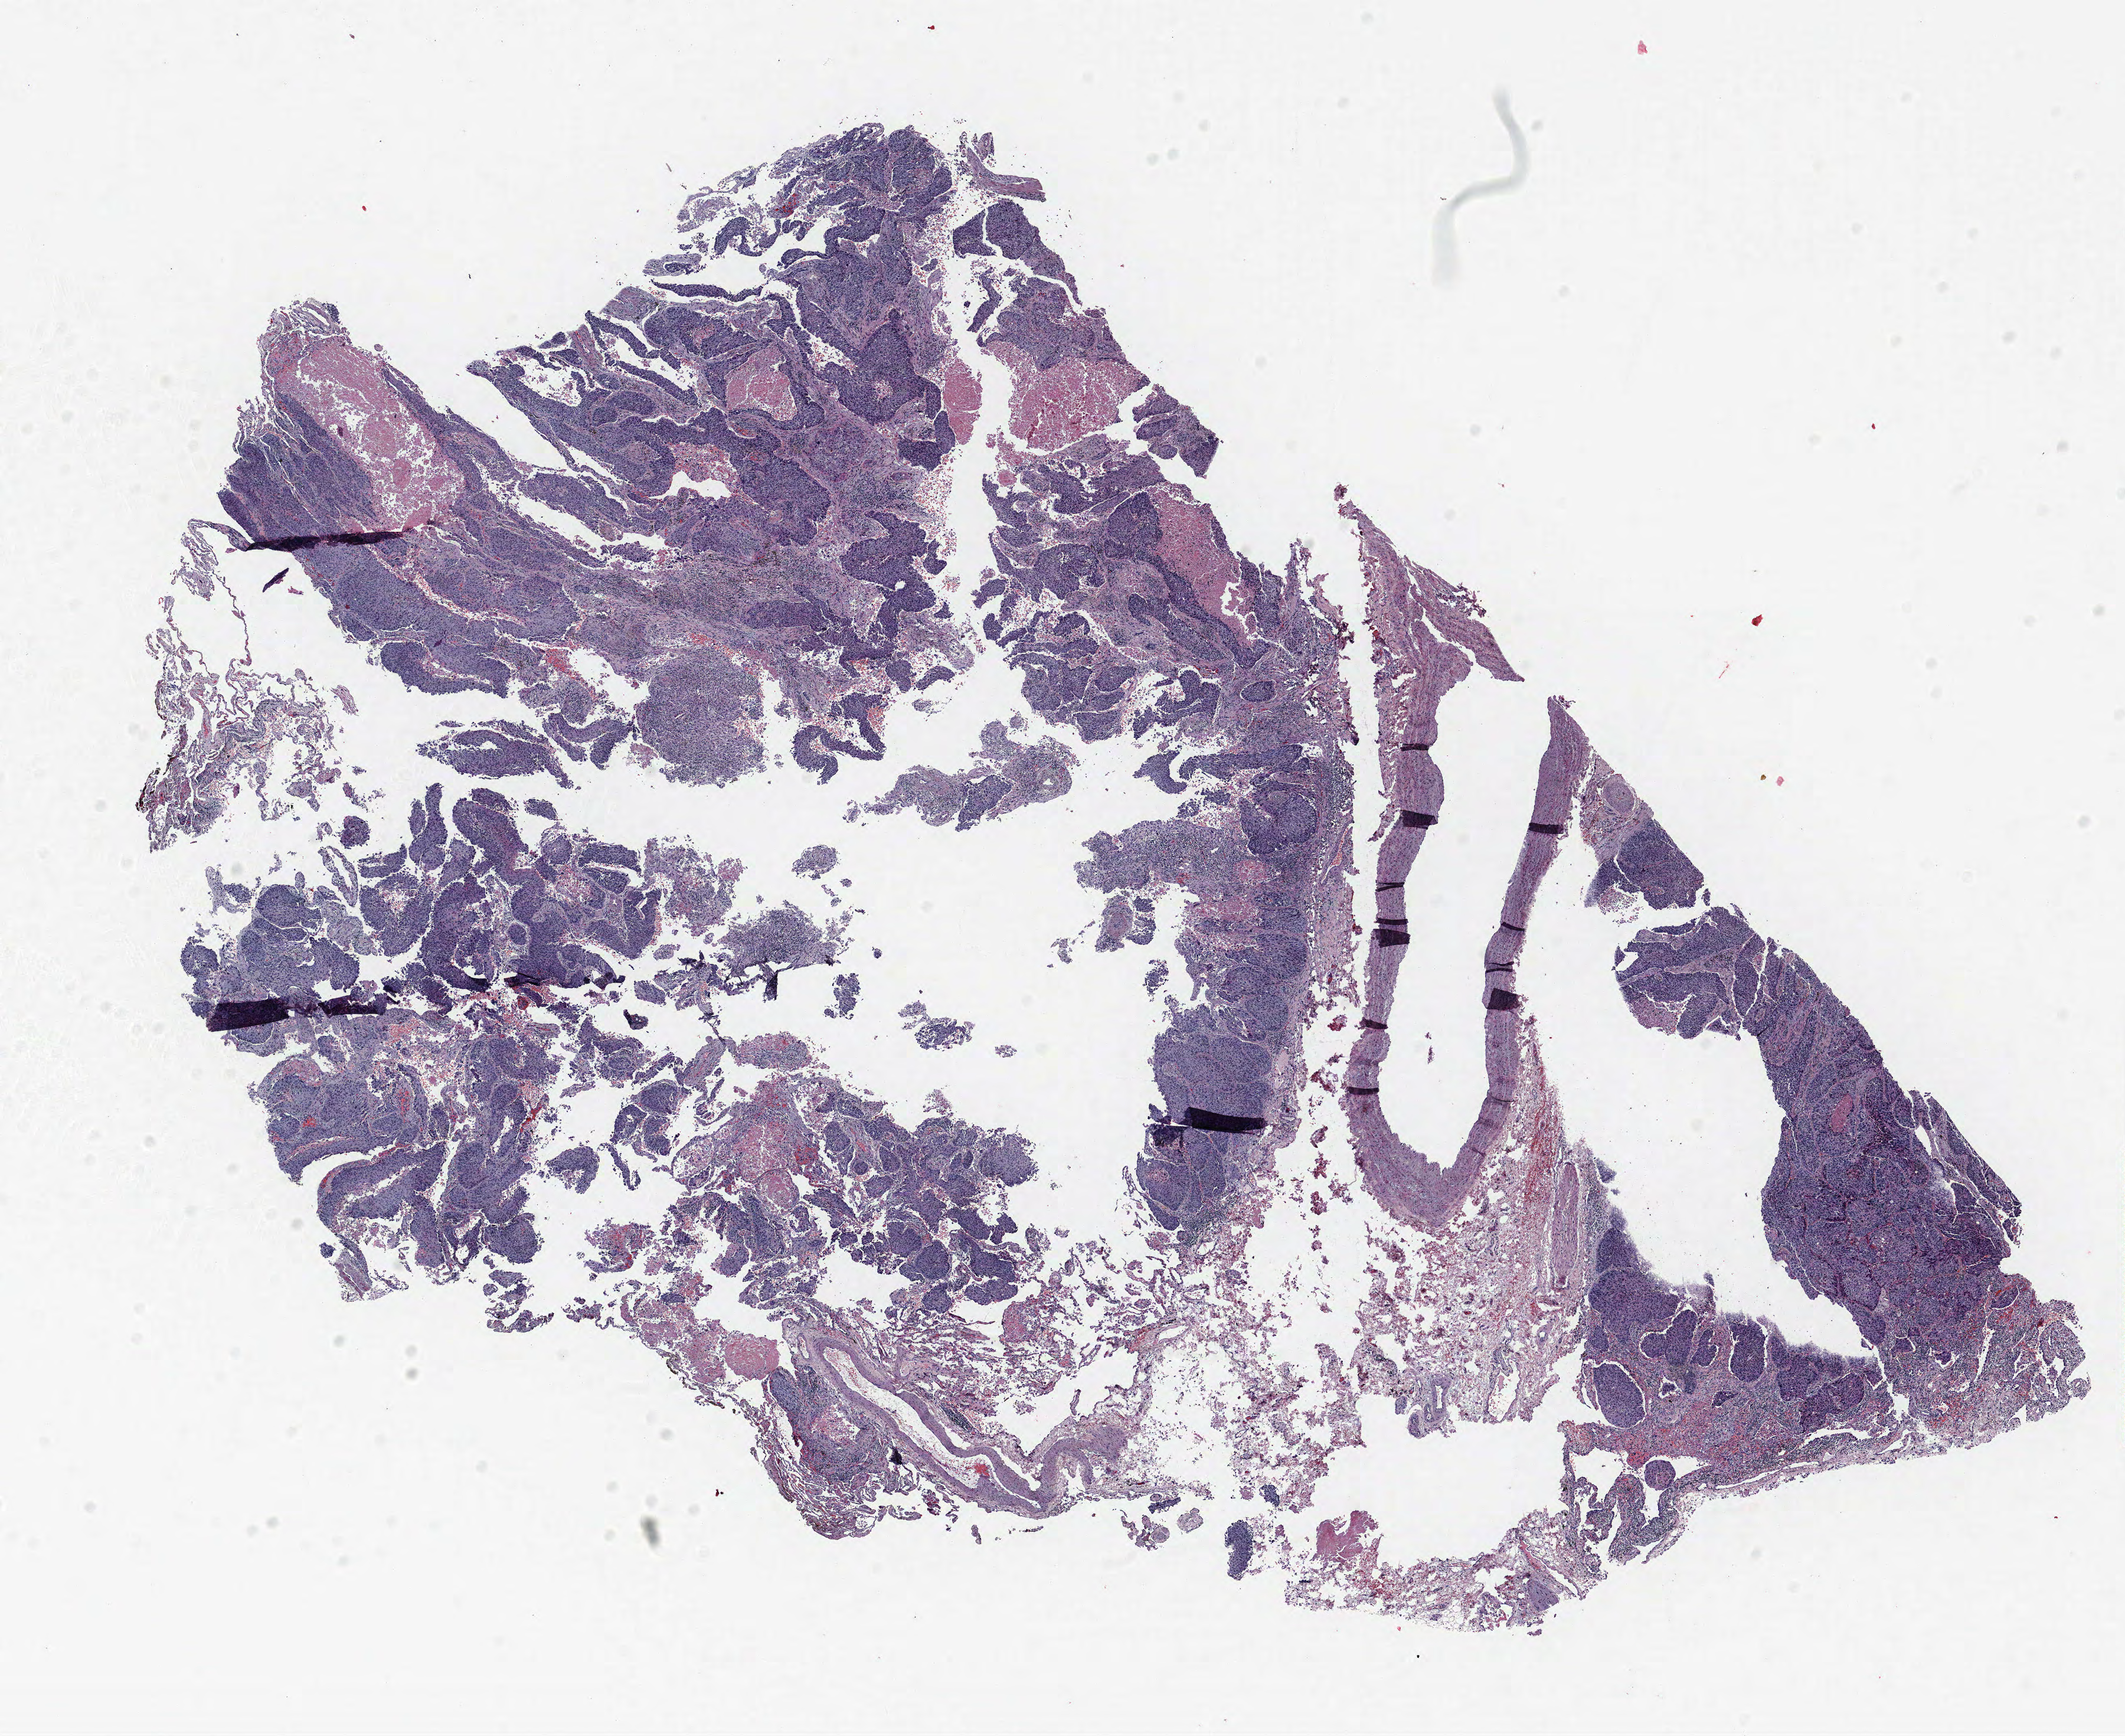
Whole-slide histology image, Hematoxylin and eosin (H&E) stained, a low-resolution overview of the entire scanned area, about 14.4 x 11.8 mm, formalin-fixed paraffin-embedded (FFPE) section, lung. Male patient, aged 65 at enrolment.
Participant's lung-cancer diagnosis: Squamous cell carcinoma, NOS (ICD-O-3 8070/3).